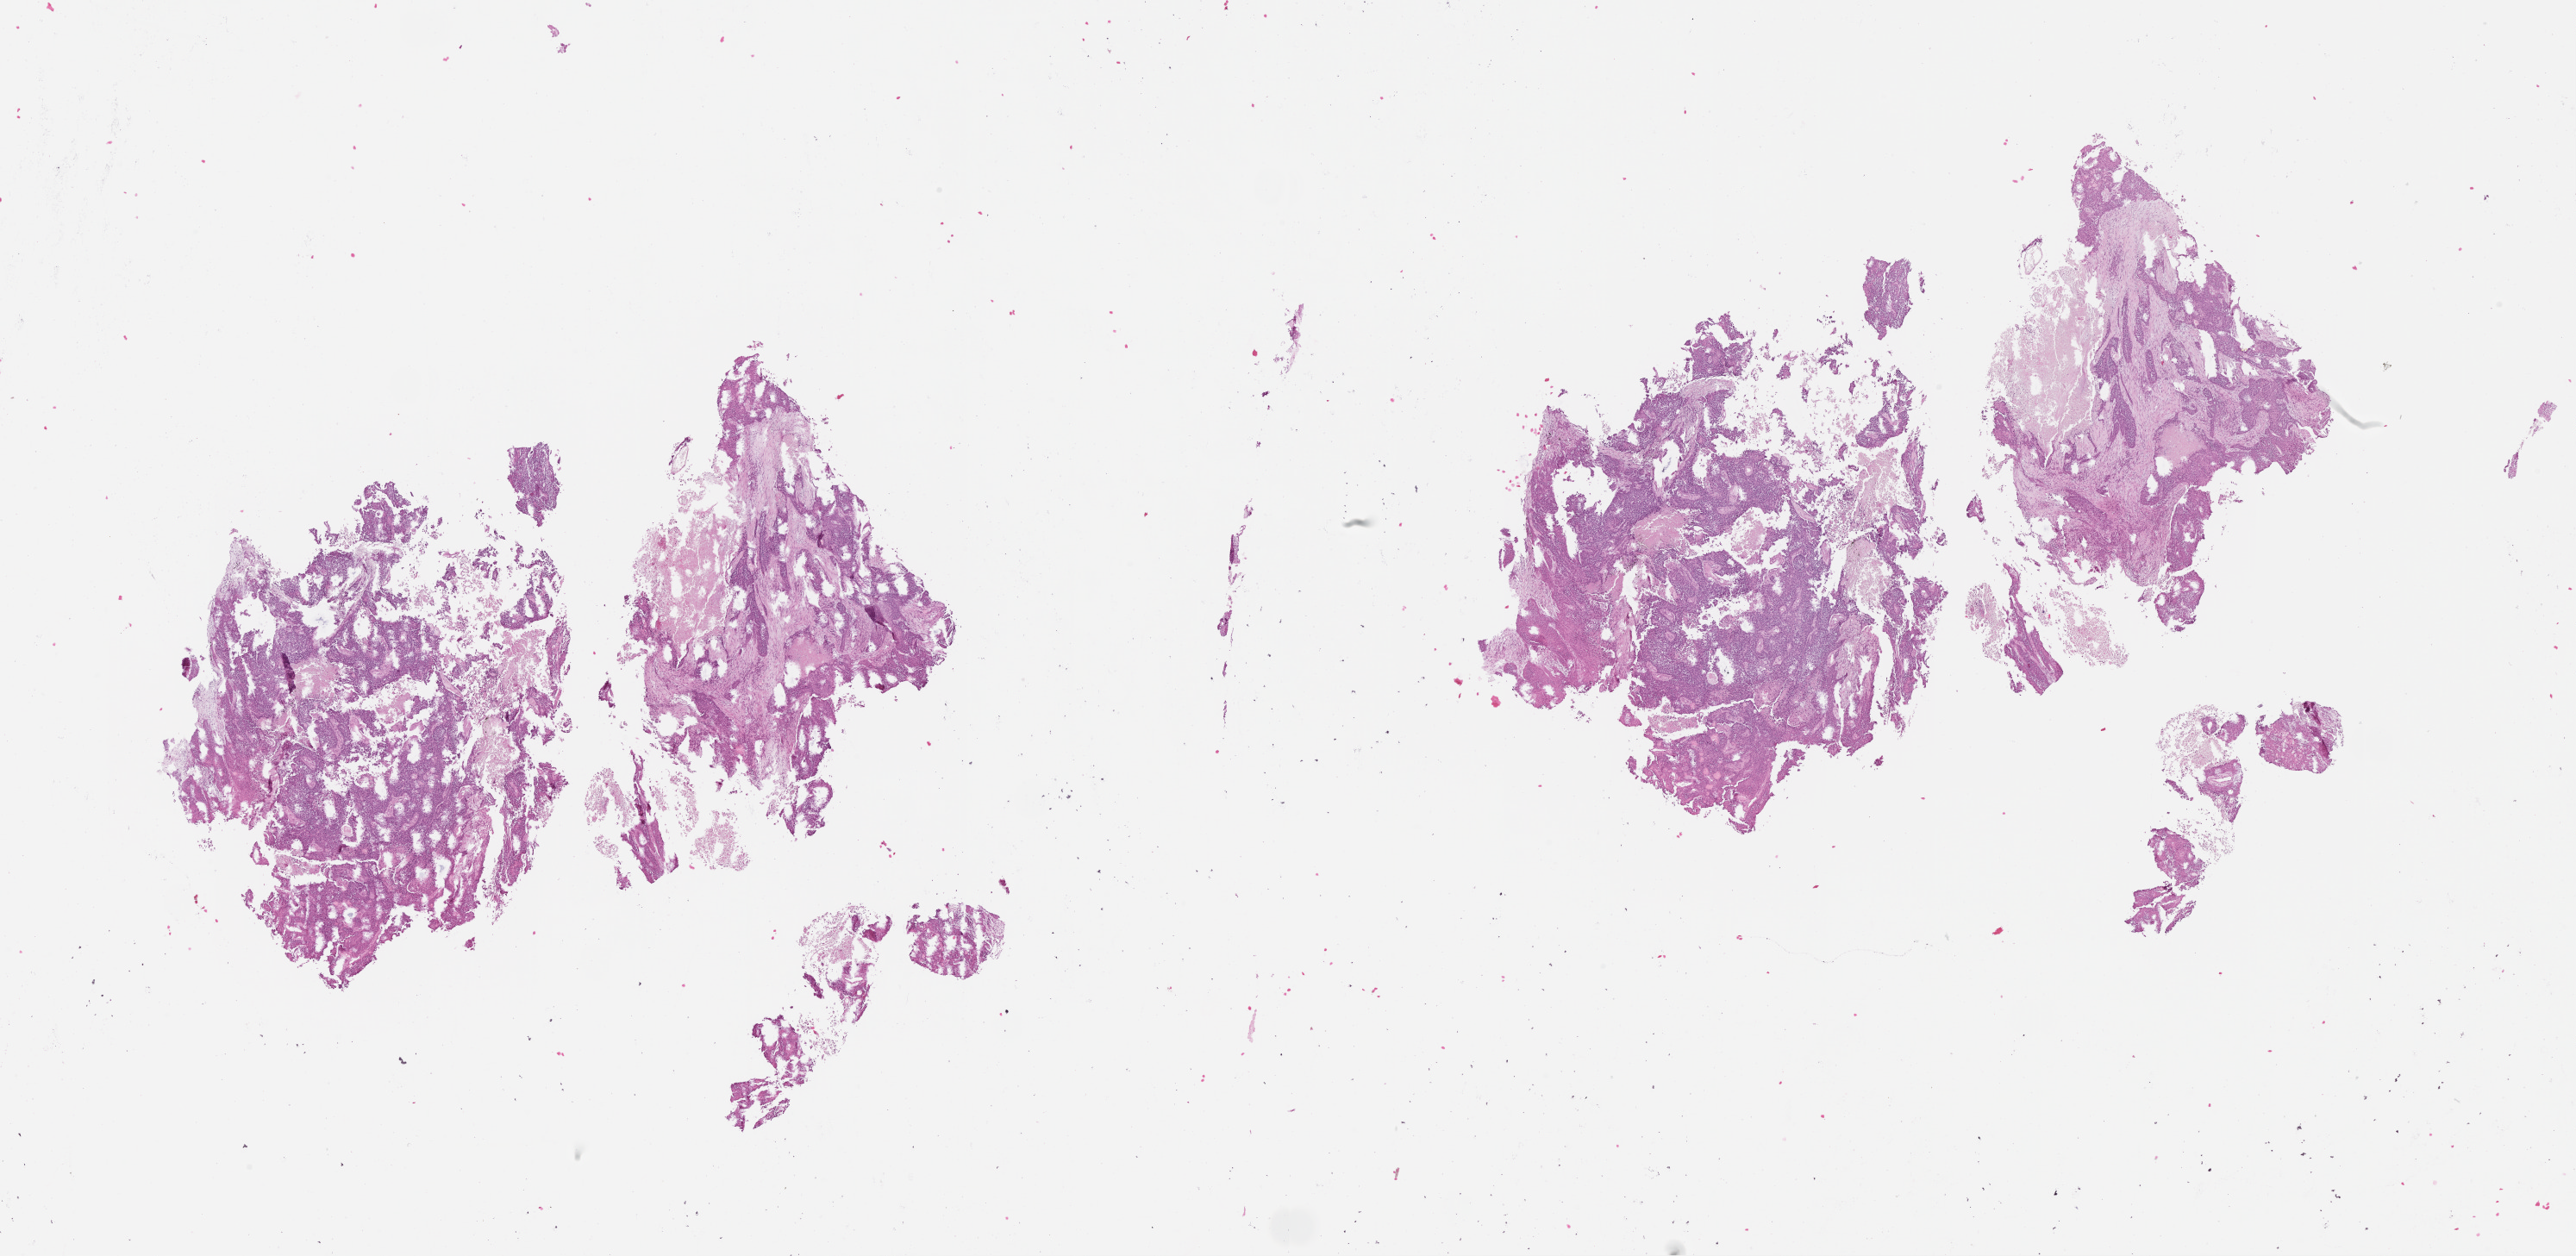
Digitized Hematoxylin and eosin (H&E) stained tissue section (whole slide) — shown as a low-resolution overview of the whole scanned area (about 24.1 x 11.7 mm). Lung, tumour tissue. Male, 66 y/o.
* patient diagnosis (cohort enrolment): squamous cell carcinoma (lung)